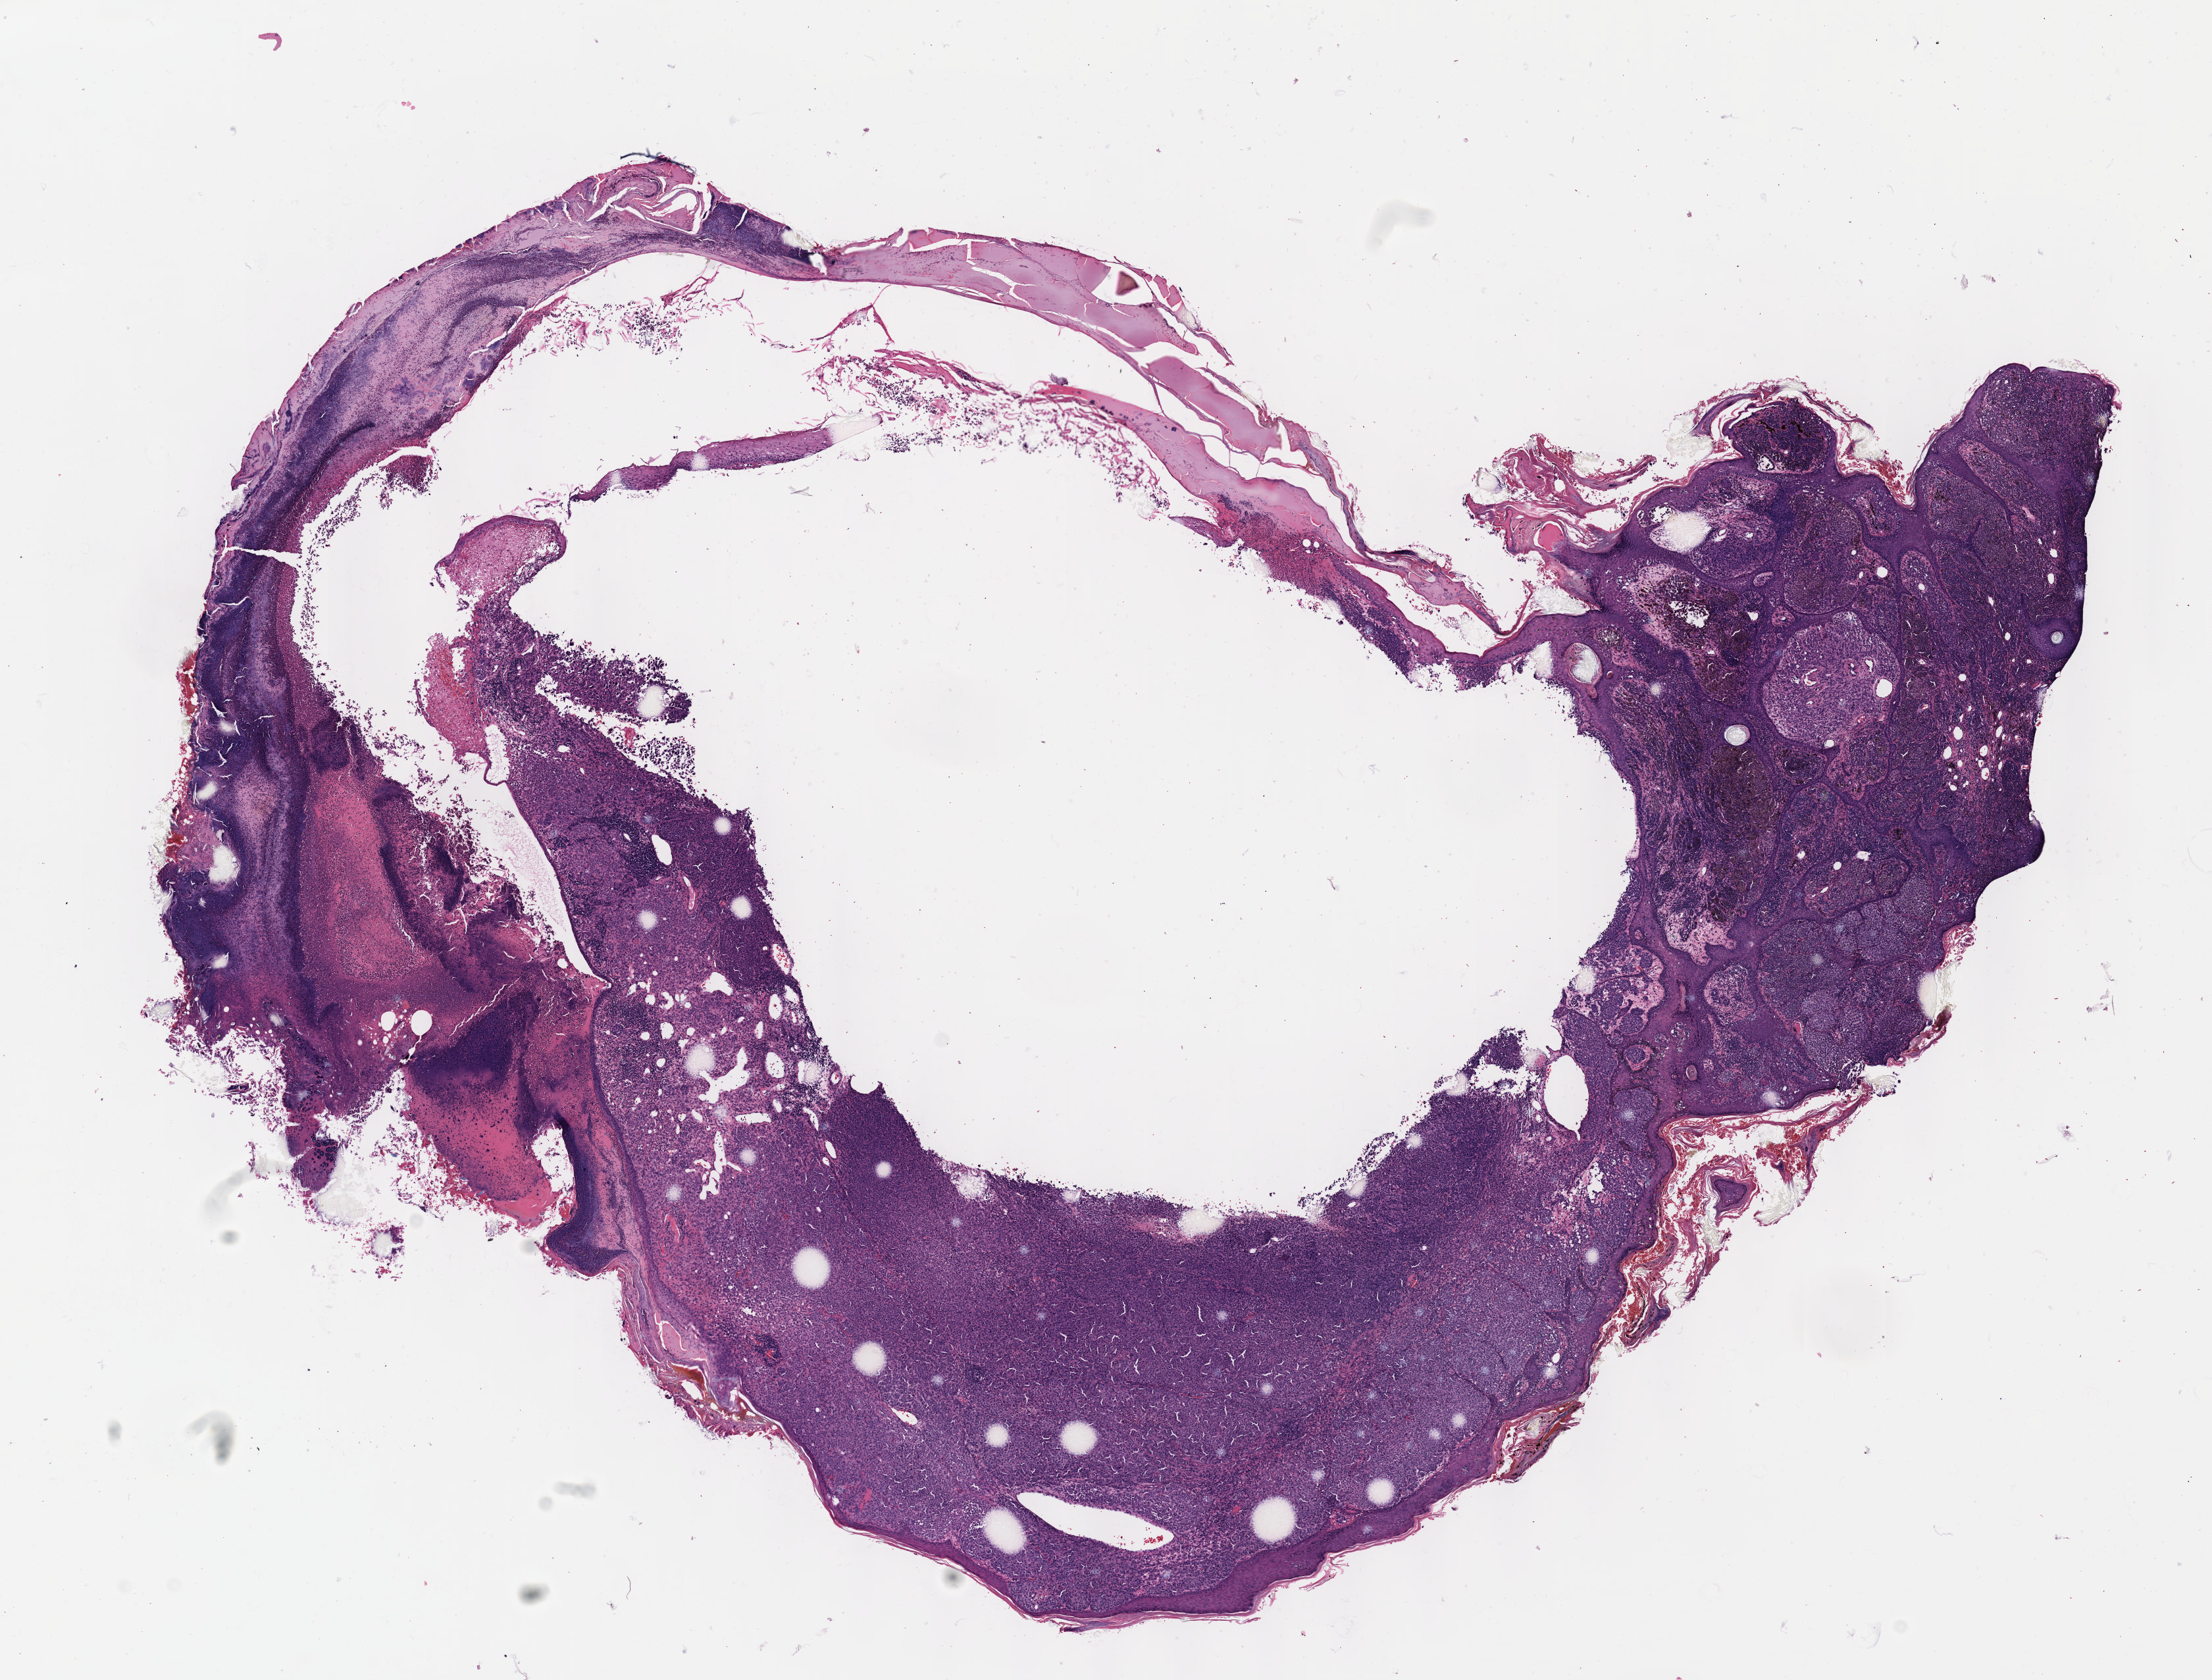
H&E-stained whole-slide image — whole scanned area (about 13.6 x 10.3 mm, slide scanned at 40x) shown as a low-resolution overview, formalin-fixed paraffin-embedded (FFPE) diagnostic section, sample: primary tumour, skin. Patient: female, age at initial diagnosis 36 years.
Diagnosis: Malignant melanoma, NOS. AJCC pathologic stage: IIIB. TNM: T4b N1 M0.